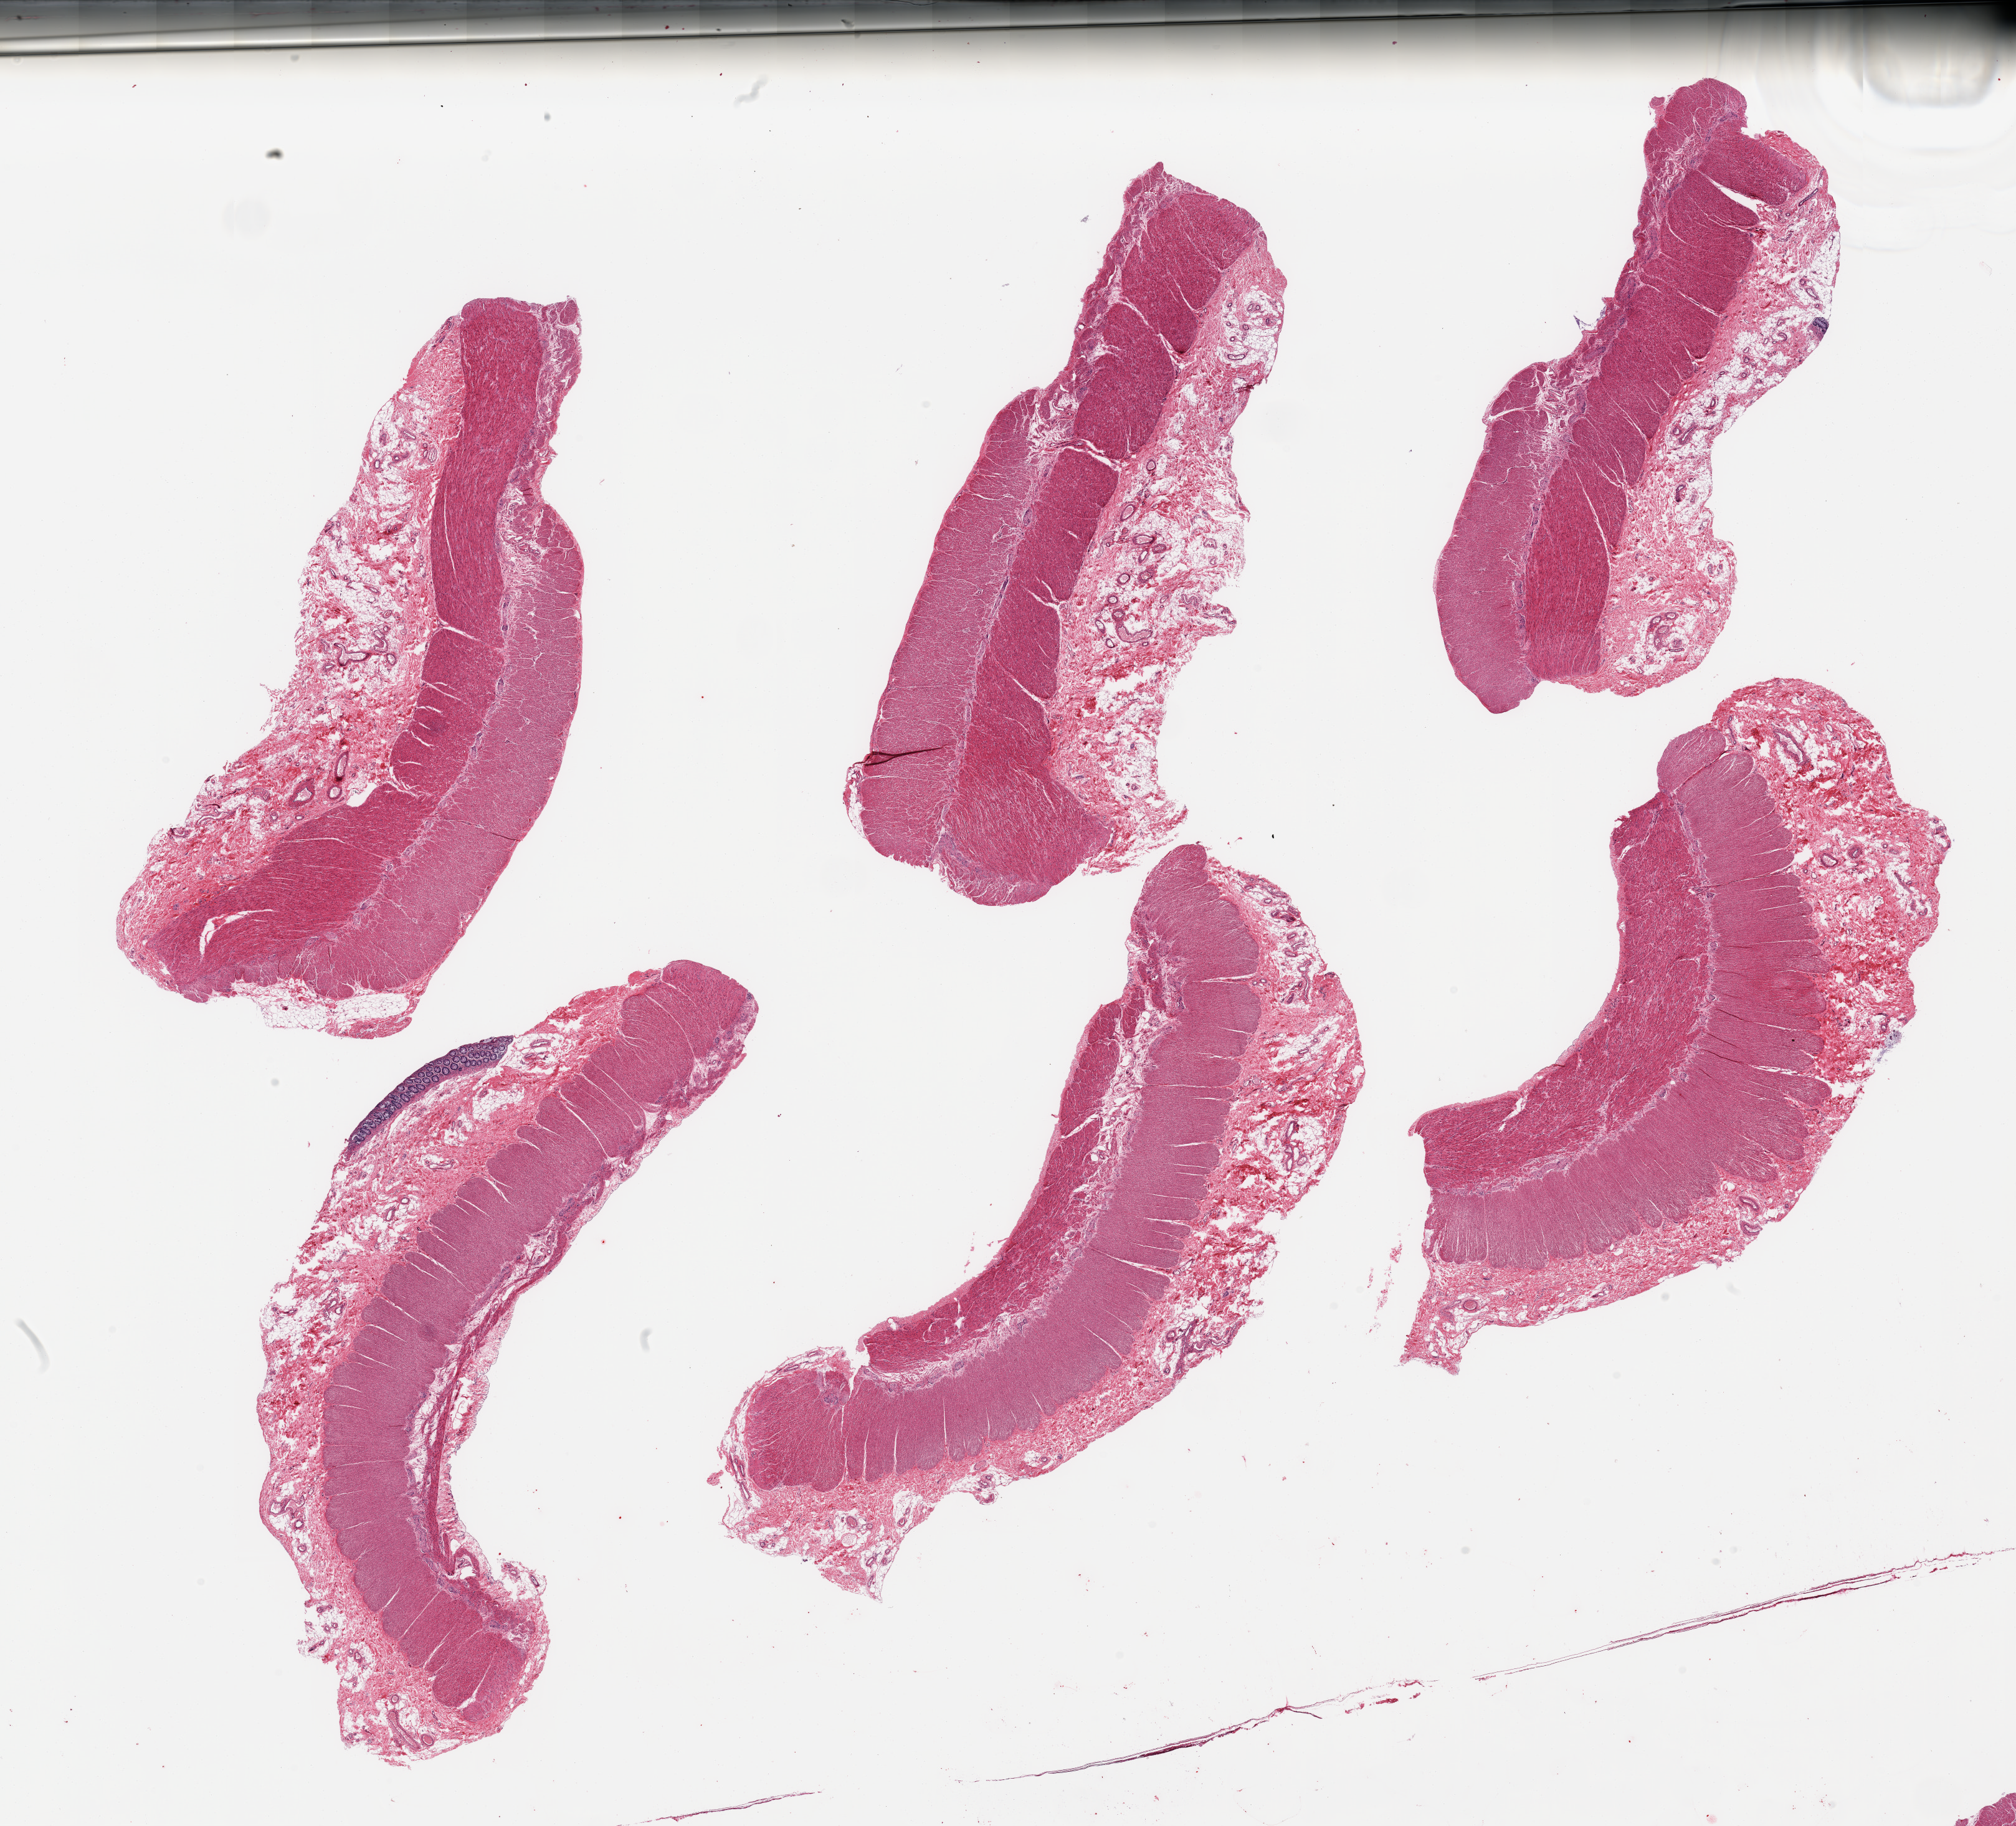
Whole-slide image, H&E stain, brightfield — a low-resolution overview of the entire scanned area, about 25.6 x 23.2 mm (from a 20x scan); PAXgene-fixed, paraffin-embedded tissue; section of sigmoid colon (target tissue); tissue donor sample. Male donor.
* review note (as recorded): 6 pieces; predominantly target muscularis, but residual submucosa and strip of mucosa